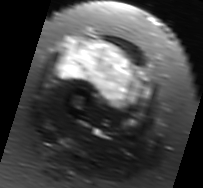
MRI of an extremity soft-tissue mass, one axial slice; position 26 of 91 along the scan axis; T2-weighted fat-saturated; MR volume resampled by the dataset authors to the PET/CT grid (not the native acquisition matrix); 3.27 mm slice thickness; 203 × 188 image matrix, field of view 198 × 184 mm. Female patient. Case-level facts recorded for this patient, not image findings: histological type: malignant solitary fibrous tumor; grade: intermediate; site of the primary tumour: right thigh.
Structures marked on this image (expert contour drawn on MRI and transferred to this co-registered scan by the dataset authors):
- gross tumour volume including surrounding oedema: bounding box [x1, y1, x2, y2] px = [56, 35, 153, 111]
- gross tumour volume (mass): [58, 42, 139, 104]